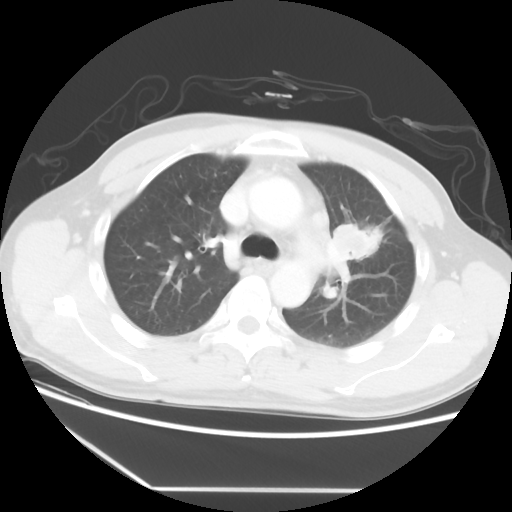
Chest CT, one axial slice. Slice 39 of 56 in the series (ordered by position). Lung window (W 1500 / L -600 HU). 5 mm slice thickness. 512 × 512 image matrix, field of view 373 × 373 mm. Patient: male, 53 years. Case-level facts recorded for this patient, not image findings: clinical TNM (as recorded): T2a N1 M1b.
Outlined on this slice (bounding box drawn by a radiologist):
- lung tumour (recorded histology: adenocarcinoma): box from (x=335, y=221) to (x=380, y=263) px